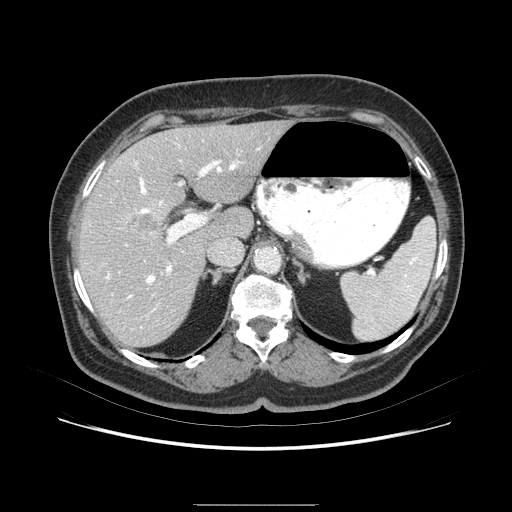
Contrast-enhanced abdominal CT (liver protocol), one axial slice. Slice 49 of 79 in the series (ordered by position). Soft-tissue window (W 400 / L 40 HU). 2.5 mm slice thickness. 512 × 512 image matrix, field of view 380 × 380 mm. Case-level facts recorded for this patient, not image findings: diagnosis: hepatocellular carcinoma (patient treated with transarterial chemoembolisation; whether this scan precedes or follows treatment is not stated here); TNM stage (as recorded): Stage-I; Child-Pugh class: A; tumour nodularity: uninodular.
Outlined on this slice (semi-automatic segmentation, software-assisted and operator-edited):
- liver parenchyma outside the tumour (the mass and vessels are separate outlines, so this box may not span the whole liver): box from (x=74, y=124) to (x=296, y=348) px
- liver vessels: (x=108, y=151)–(x=260, y=295)